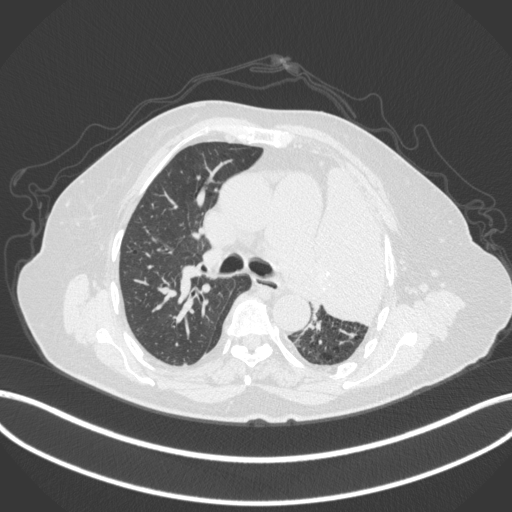
Chest CT, one axial slice. Position 249 of 399 along the scan axis. Lung window (W 1500 / L -600 HU). 1 mm slice thickness. 512 × 512 image matrix, field of view 400 × 400 mm. Female patient, age 75 years. Case-level facts recorded for this patient, not image findings: clinical TNM (as recorded): T3 N3 M1.
Annotated regions visible in this slice (rectangle marked by the reading radiologist):
- lung tumour (recorded histology: adenocarcinoma): bounding box [x1, y1, x2, y2] px = [312, 158, 402, 330]